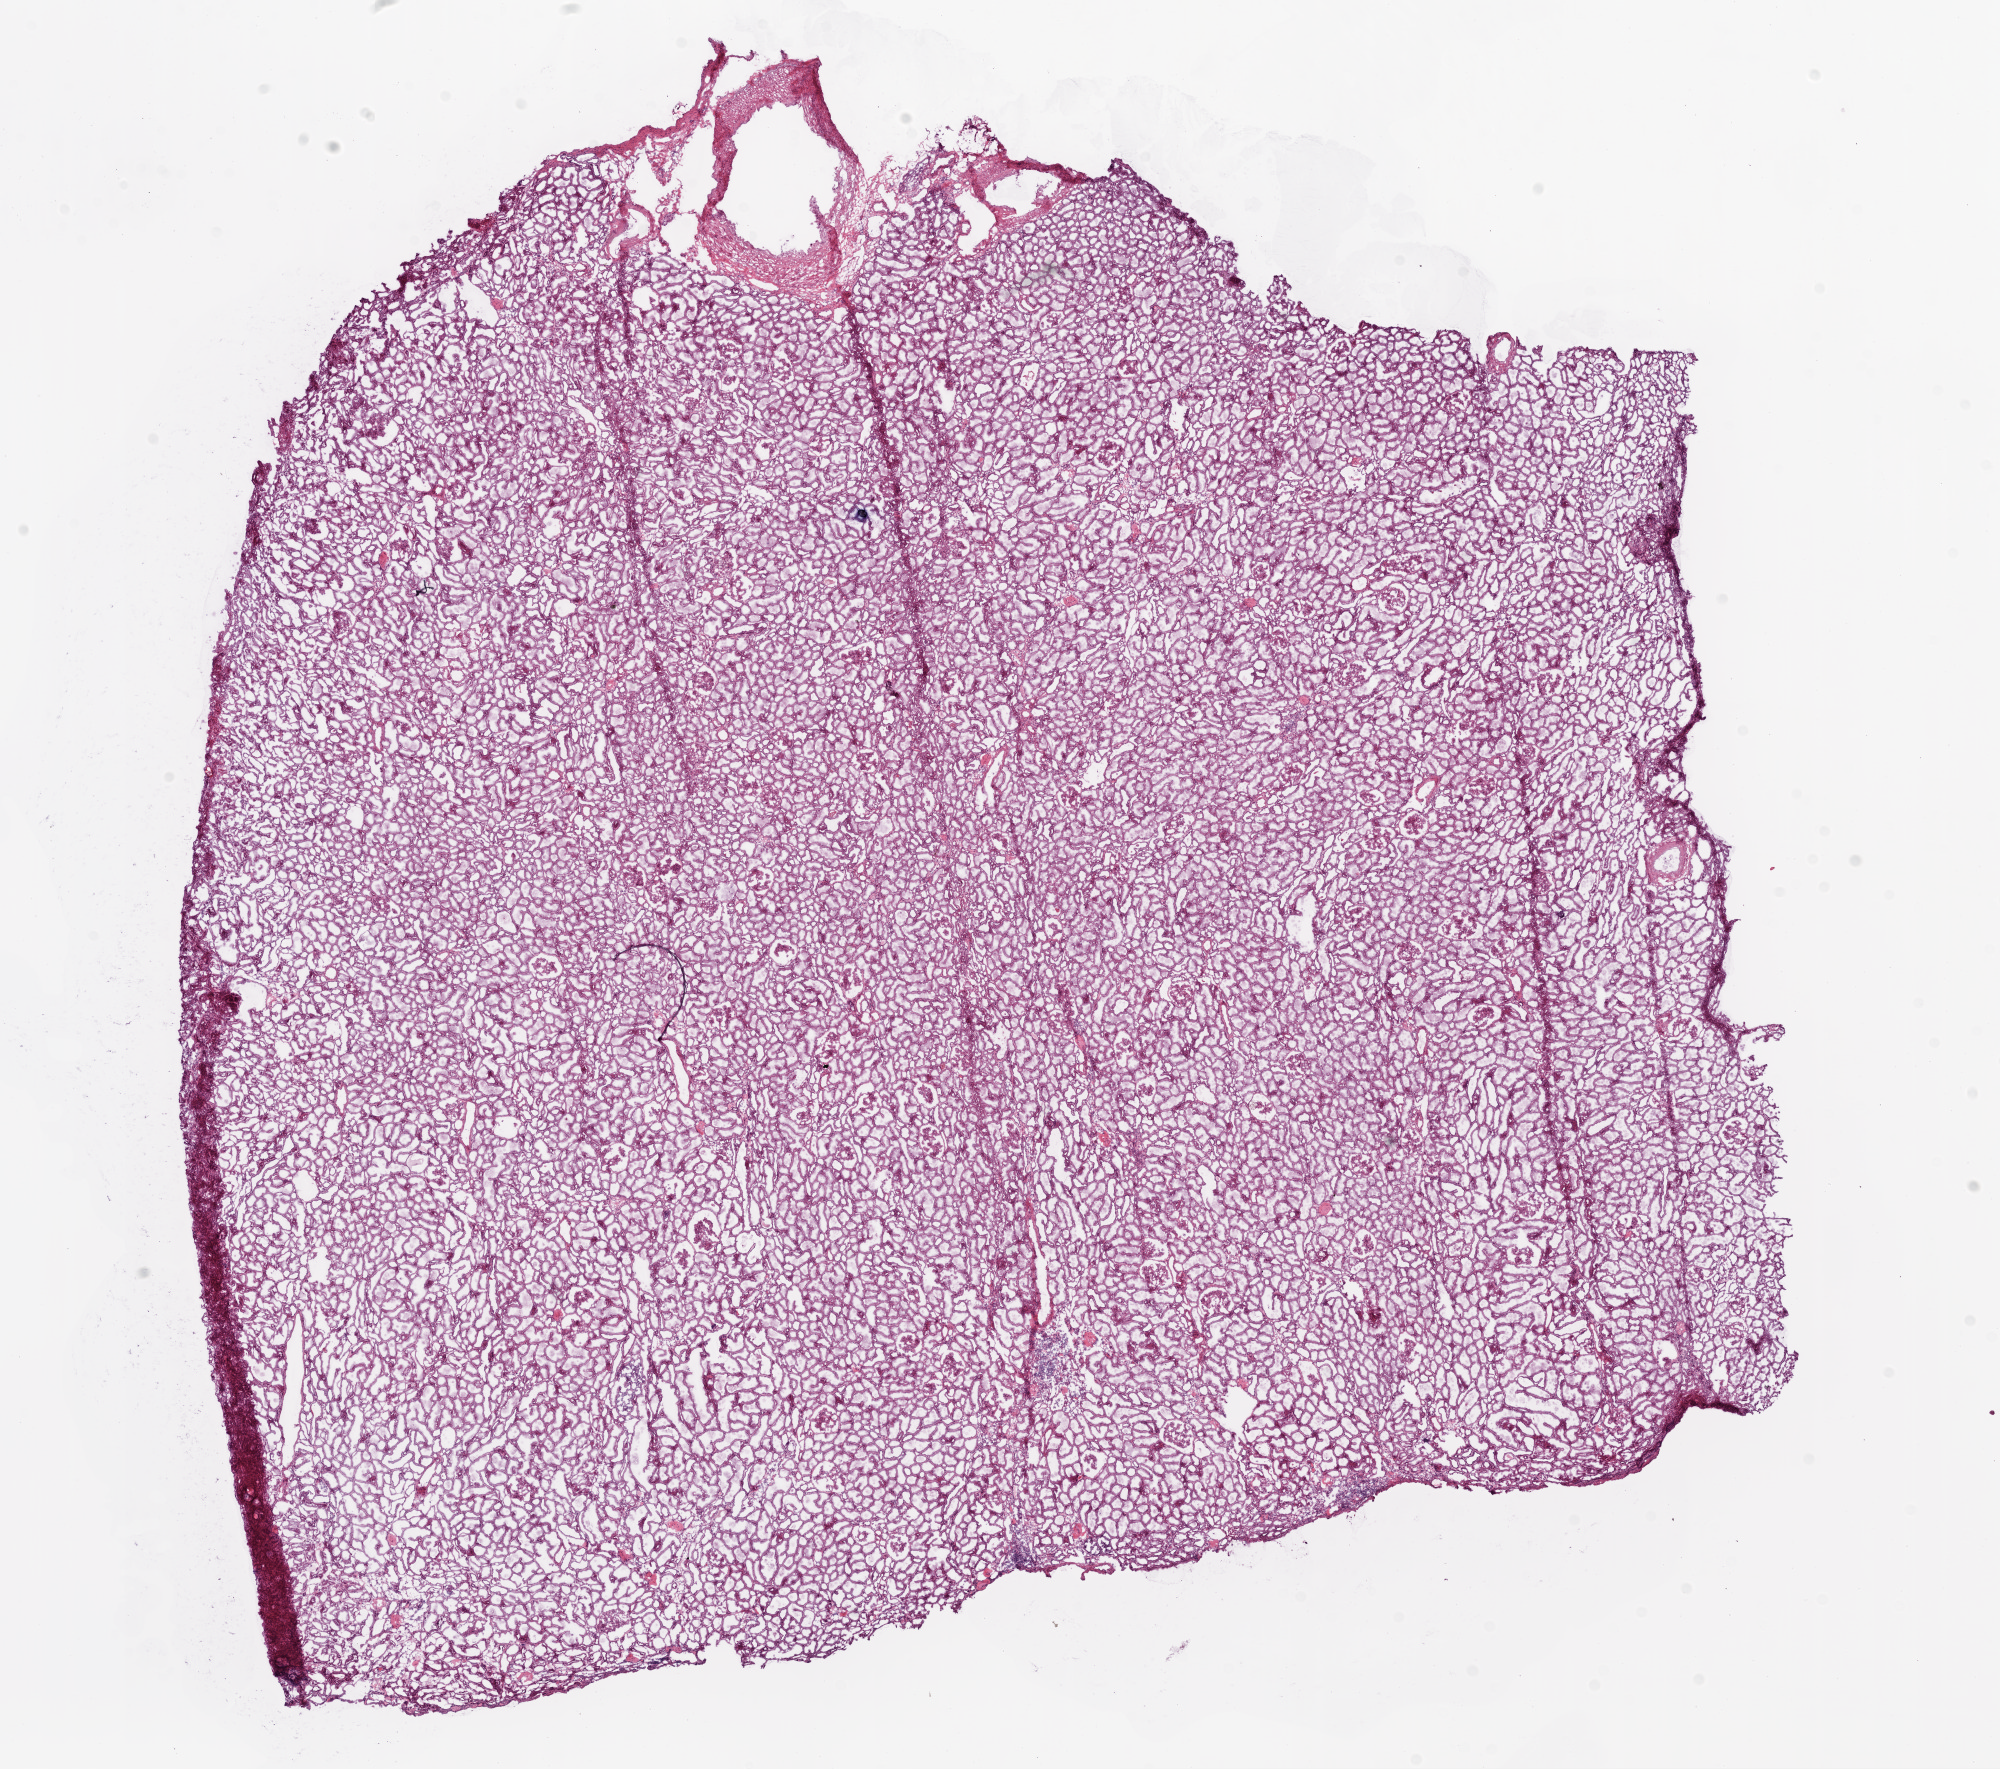
Whole-slide histology image, Hematoxylin and eosin (H&E) stained — a low-resolution overview of the entire scanned area, about 16.0 x 14.2 mm (from a 20x scan); frozen section from the bottom of the tissue portion; ovary, solid tissue normal (non-tumour tissue) sample. Female patient; age at initial diagnosis 71 years.
This section: solid tissue normal sample (biorepository sample class). Patient diagnosis: Serous cystadenocarcinoma, NOS.